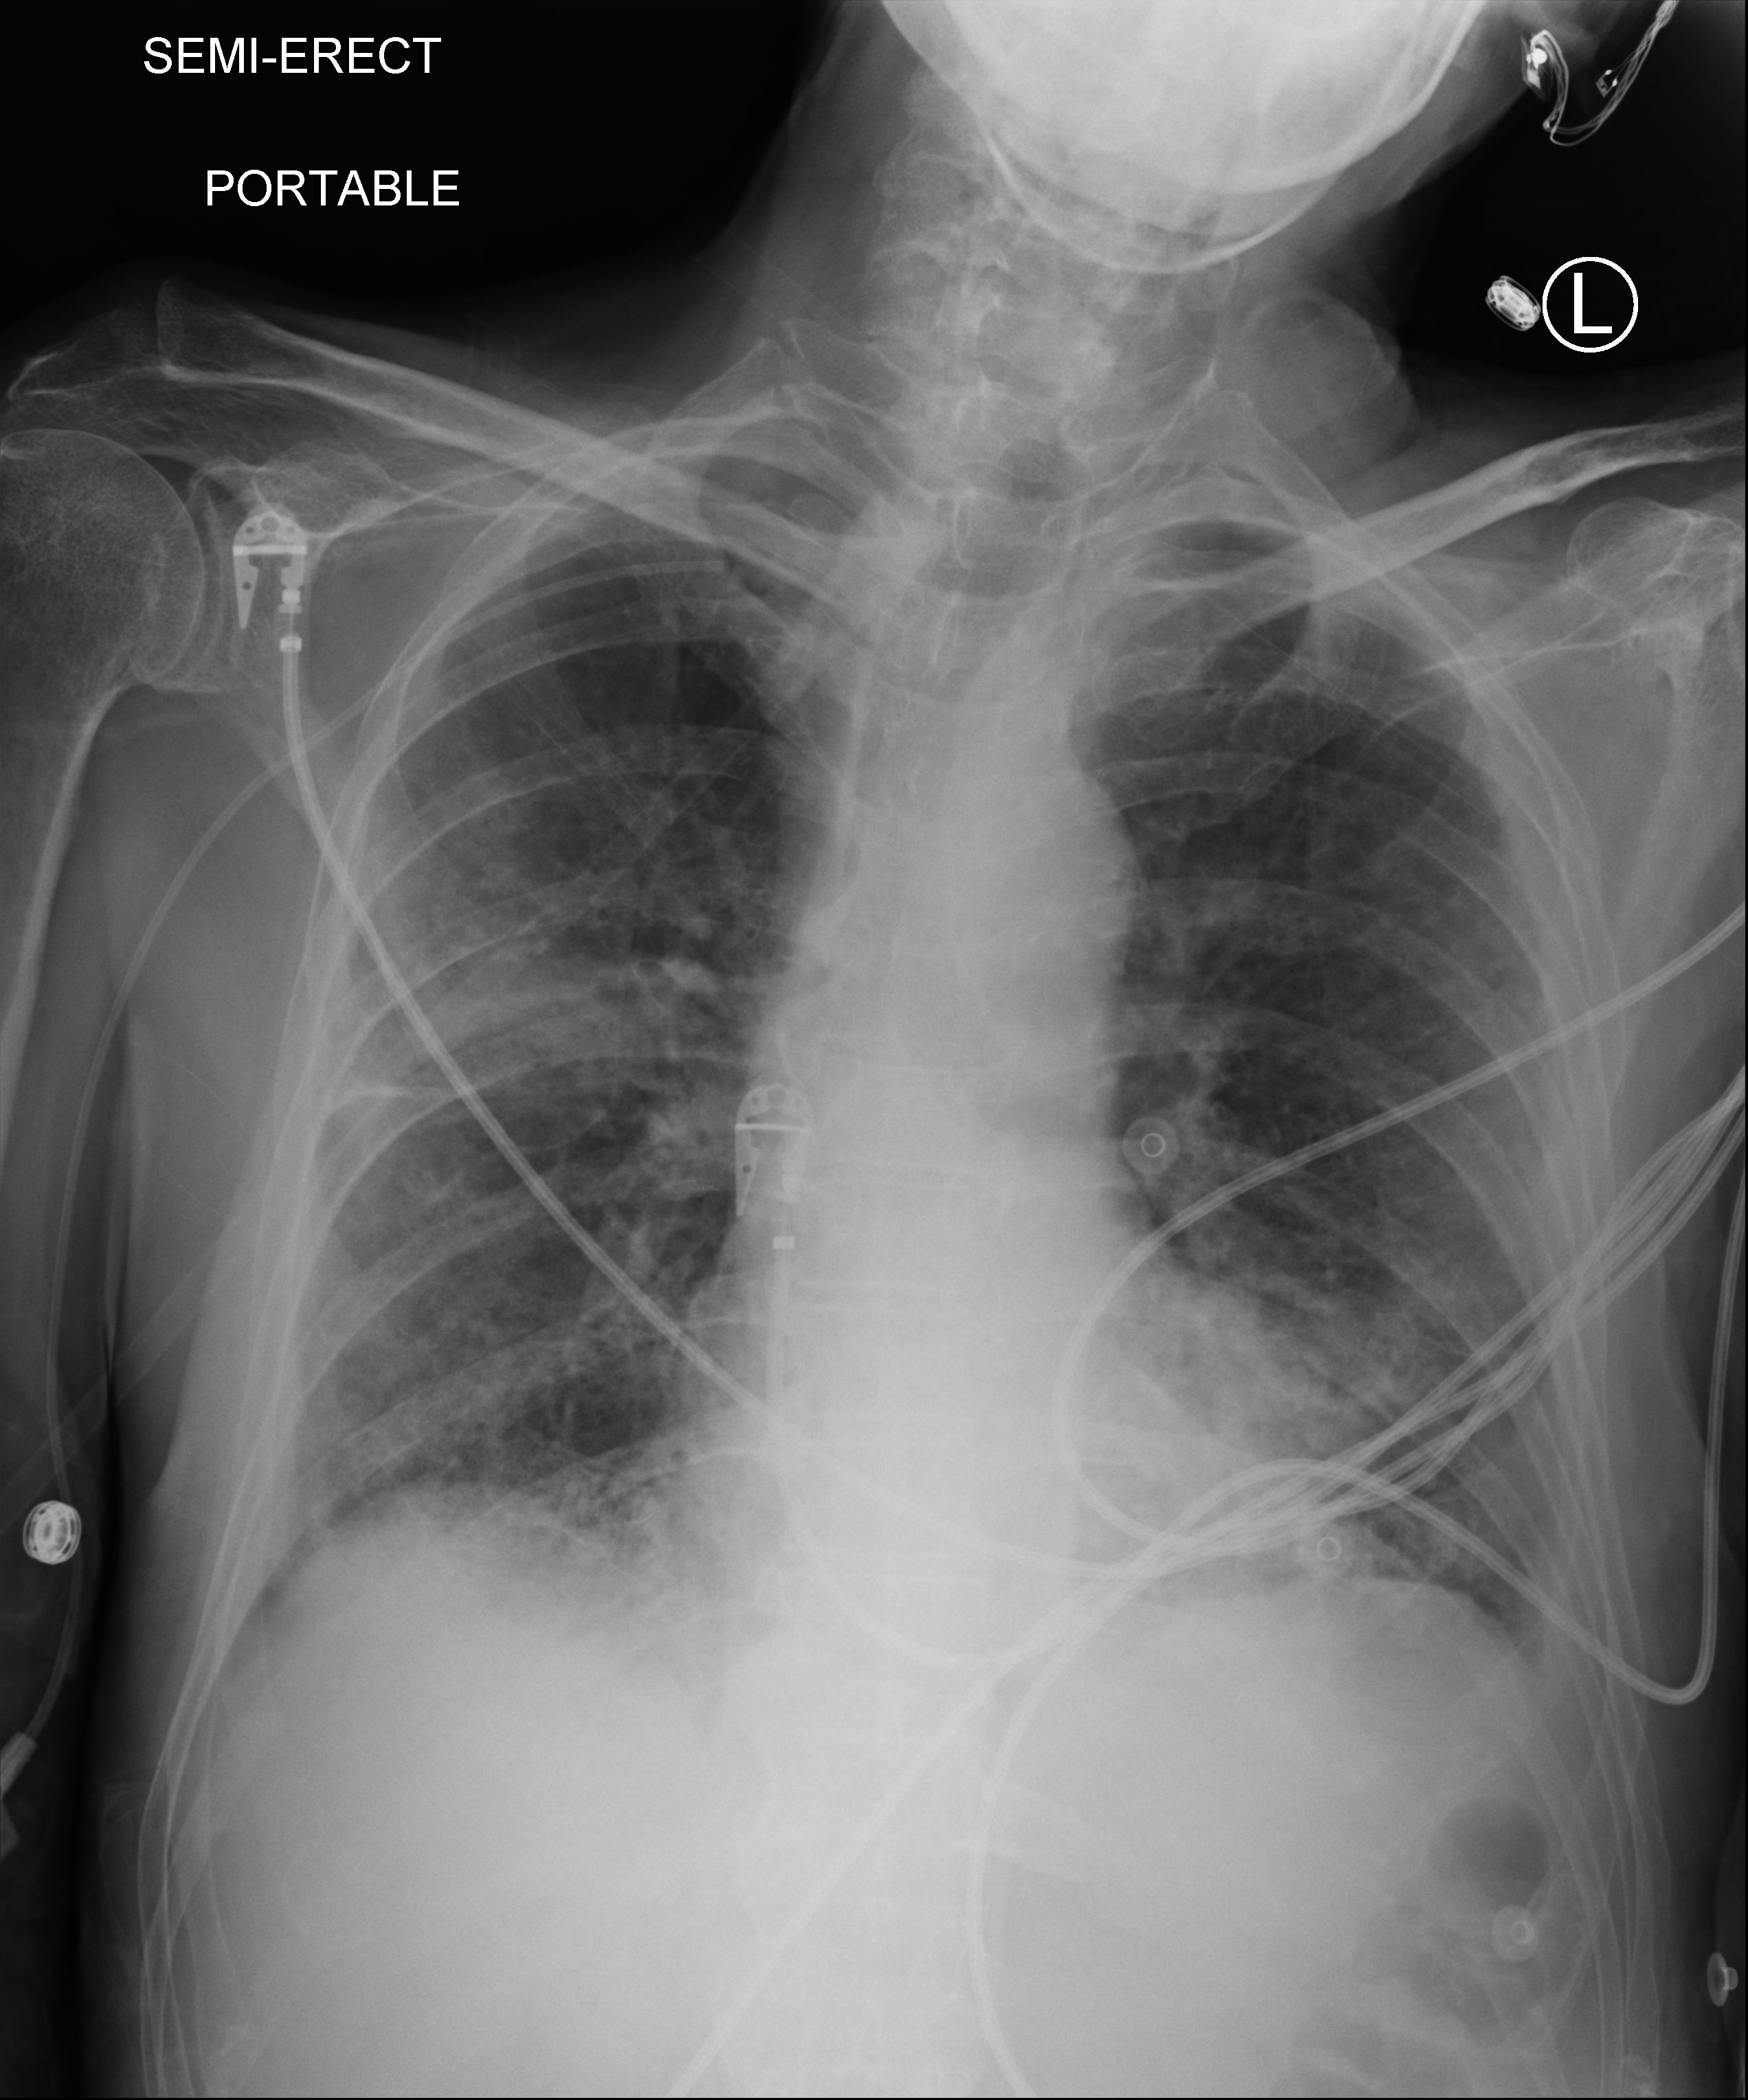
Chest X-ray (portable); anteroposterior (AP) projection. Patient hospitalised with COVID-19; male, aged 60–74 years.
Admission-level facts for this patient (not findings on this image; timing relative to this image not recorded): hypertension (admission record): yes; other chronic lung disease (admission record): no.